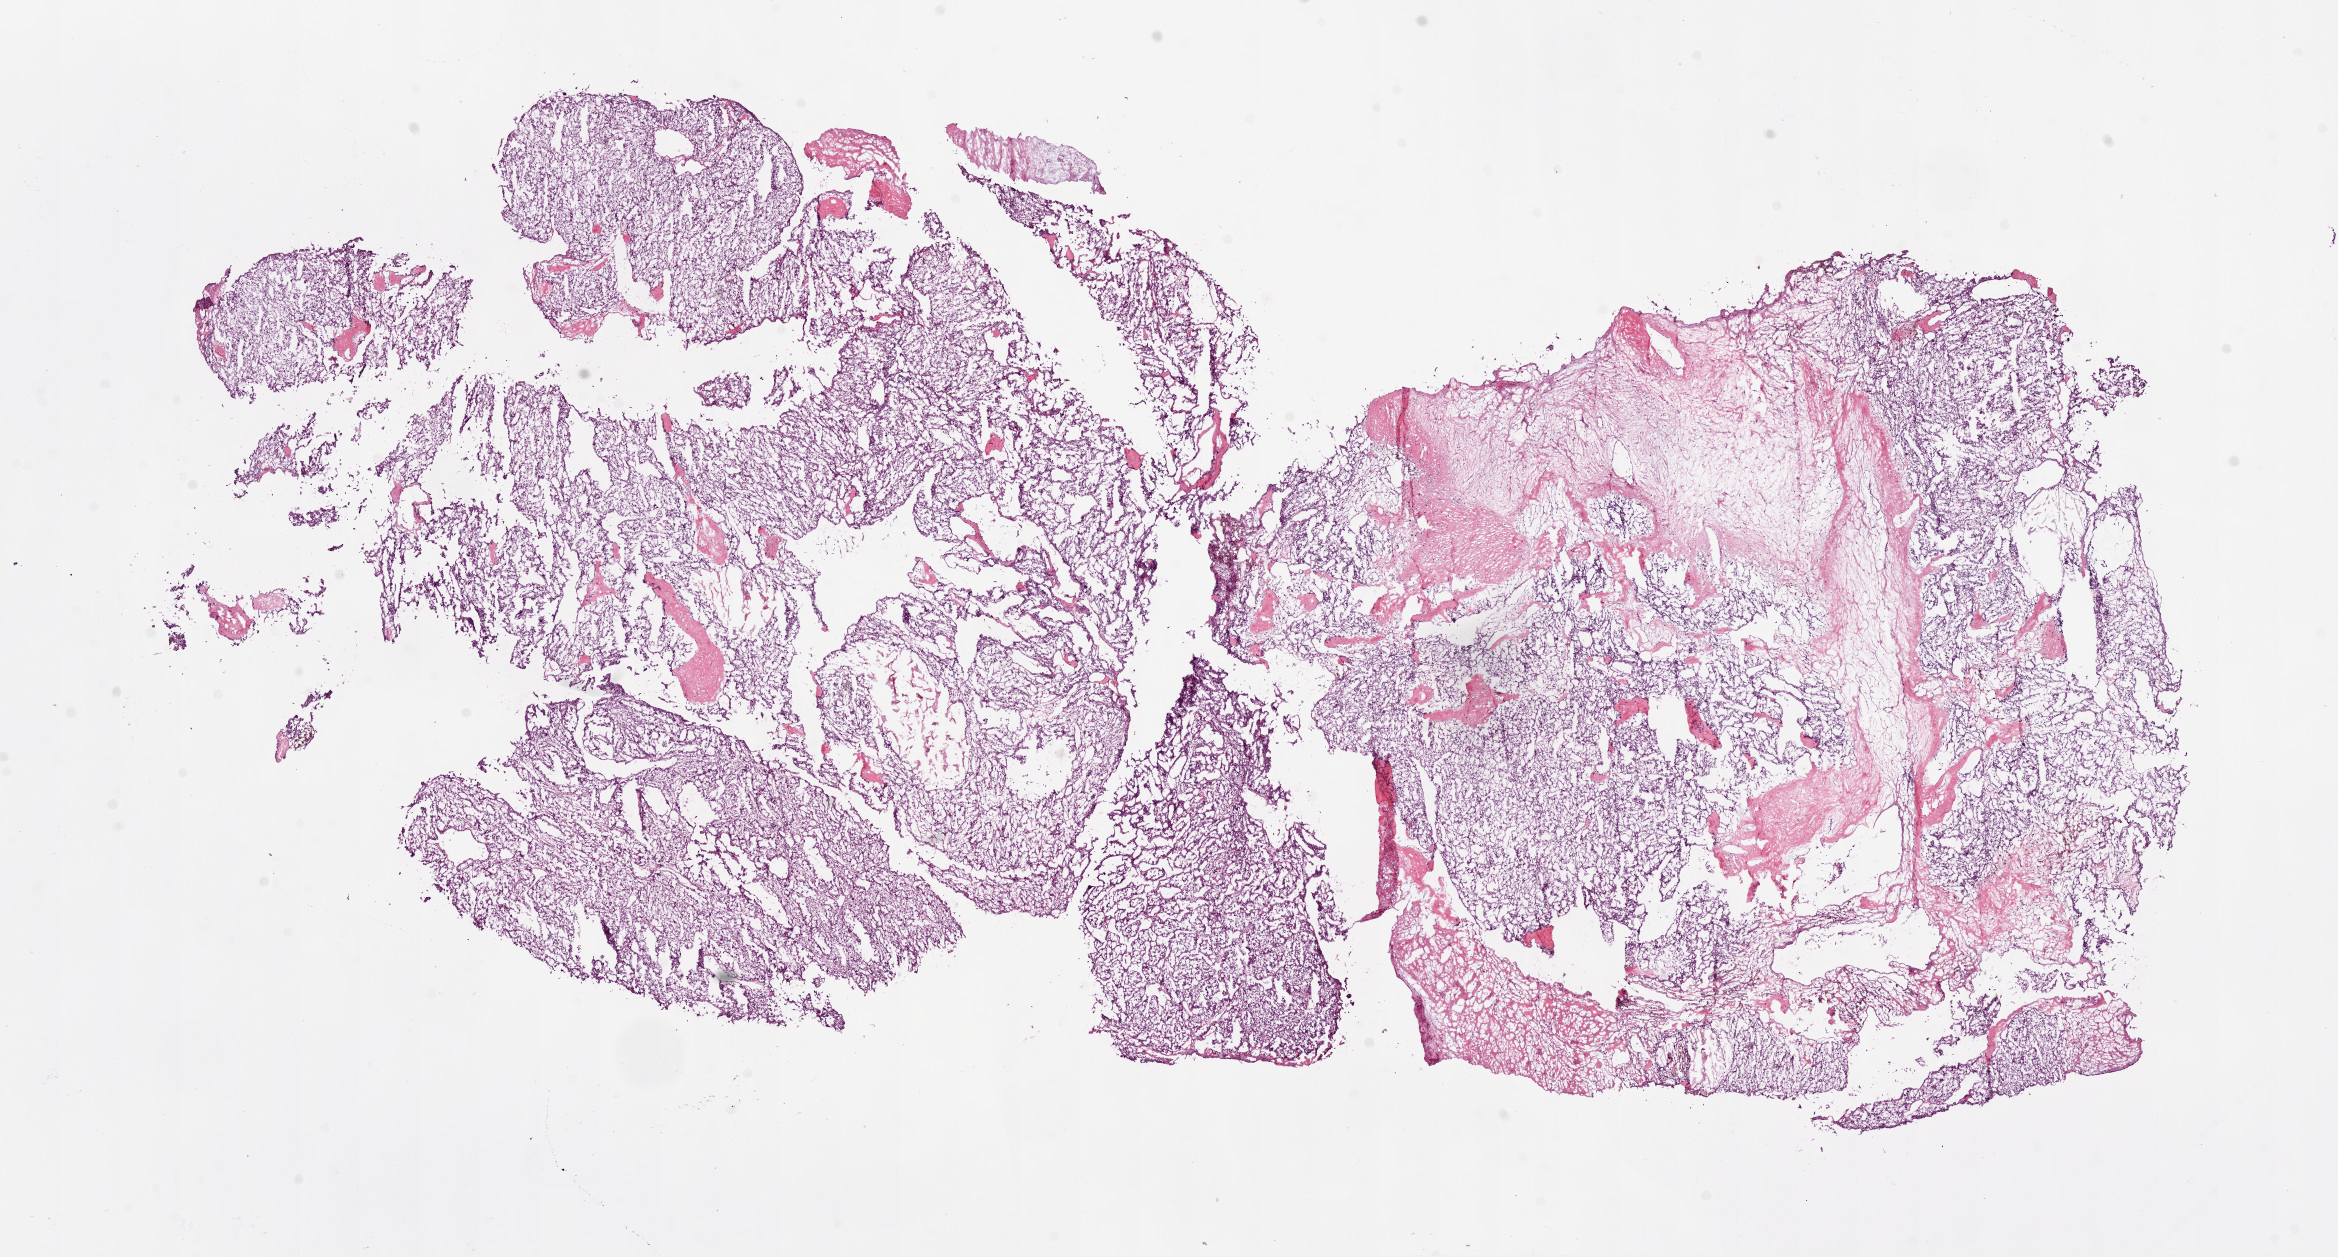
H&E-stained whole-slide image — low-resolution overview of the scanned area, about 18.9 x 10.1 mm (from a 20x scan); frozen section from the bottom of the tissue portion; kidney, primary tumour sample. Patient: male, age at initial diagnosis 47 years. Histologic grade: G3 (poorly differentiated). Slide review estimates, as recorded: tumour cells 80%, tumour nuclei 85%, normal cells 0%, stromal cells 20%, necrosis 0%.
* AJCC pathologic stage: III (7th edition)
* laterality: right
* diagnosis: Clear cell adenocarcinoma, NOS
* TNM: T3b NX M0